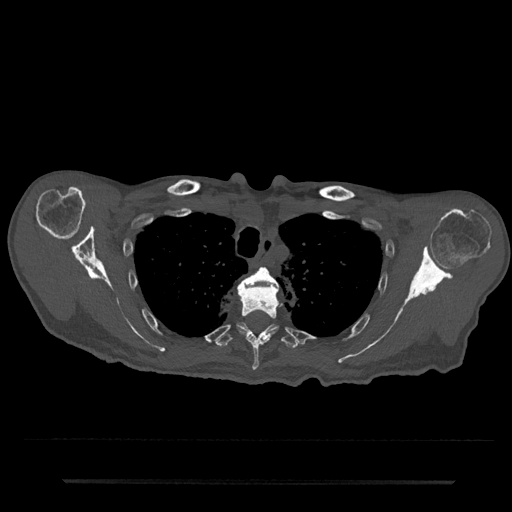
CT including the spine, one axial slice; reconstruction kernel Br40s/3; 120 kVp; bone window (W 1800 / L 400 HU); 0.5 mm slice thickness; 512 × 512 image matrix, field of view 427 × 427 mm. Patient: male, 74 years. Case-level facts recorded for this patient, not image findings: primary cancer: prostate.
Outlined on this slice (semi-automatically segmented with operator editing):
- T3 vertebra: bounding box [x1, y1, x2, y2] px = [240, 266, 279, 290]
- T4 vertebra: [238, 284, 280, 370]
- T5 vertebra: [215, 322, 300, 349]